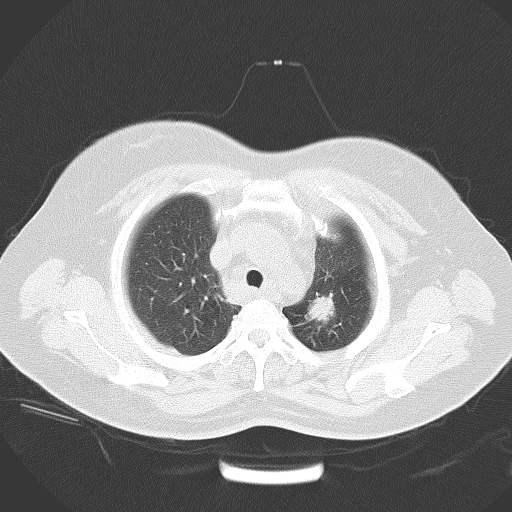
Chest CT, one axial slice; slice 49 of 58 in the series (ordered by position); lung window (W 1500 / L -600 HU); 5 mm slice thickness; 512 × 512 image matrix, field of view 390 × 390 mm. Female patient, age 53 years. From the clinical record (not read from this slice): clinical TNM (as recorded): T1c N3 M0.
Annotated regions visible in this slice (bounding box drawn by a radiologist):
- lung tumour (recorded histology: adenocarcinoma): bounding box [x1, y1, x2, y2] px = [308, 290, 340, 333]